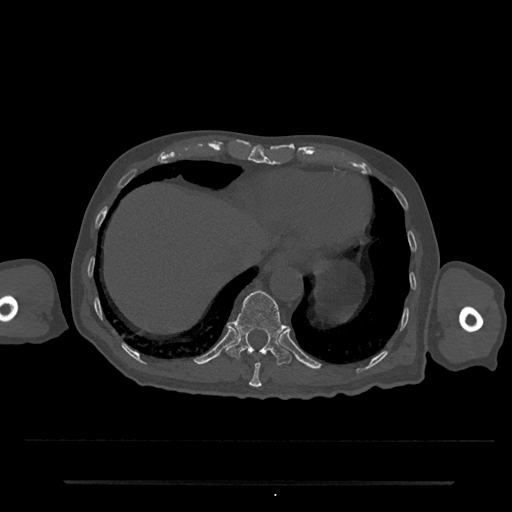
CT including the spine, one axial slice. Slice 270 of 797 in the series (ordered by position). 120 kVp. Bone window (W 1800 / L 400 HU). 0.5 mm slice thickness. 512 × 512 image matrix, field of view 427 × 427 mm. Patient: male, 74 years. Case-level facts recorded for this patient, not image findings: primary cancer: prostate.
Structures marked on this image (semi-automatic segmentation, software-assisted and operator-edited):
- T10 vertebra: bounding box <249,362,262,388> (left, top, right, bottom; pixels)
- T11 vertebra: <226,290,292,366>